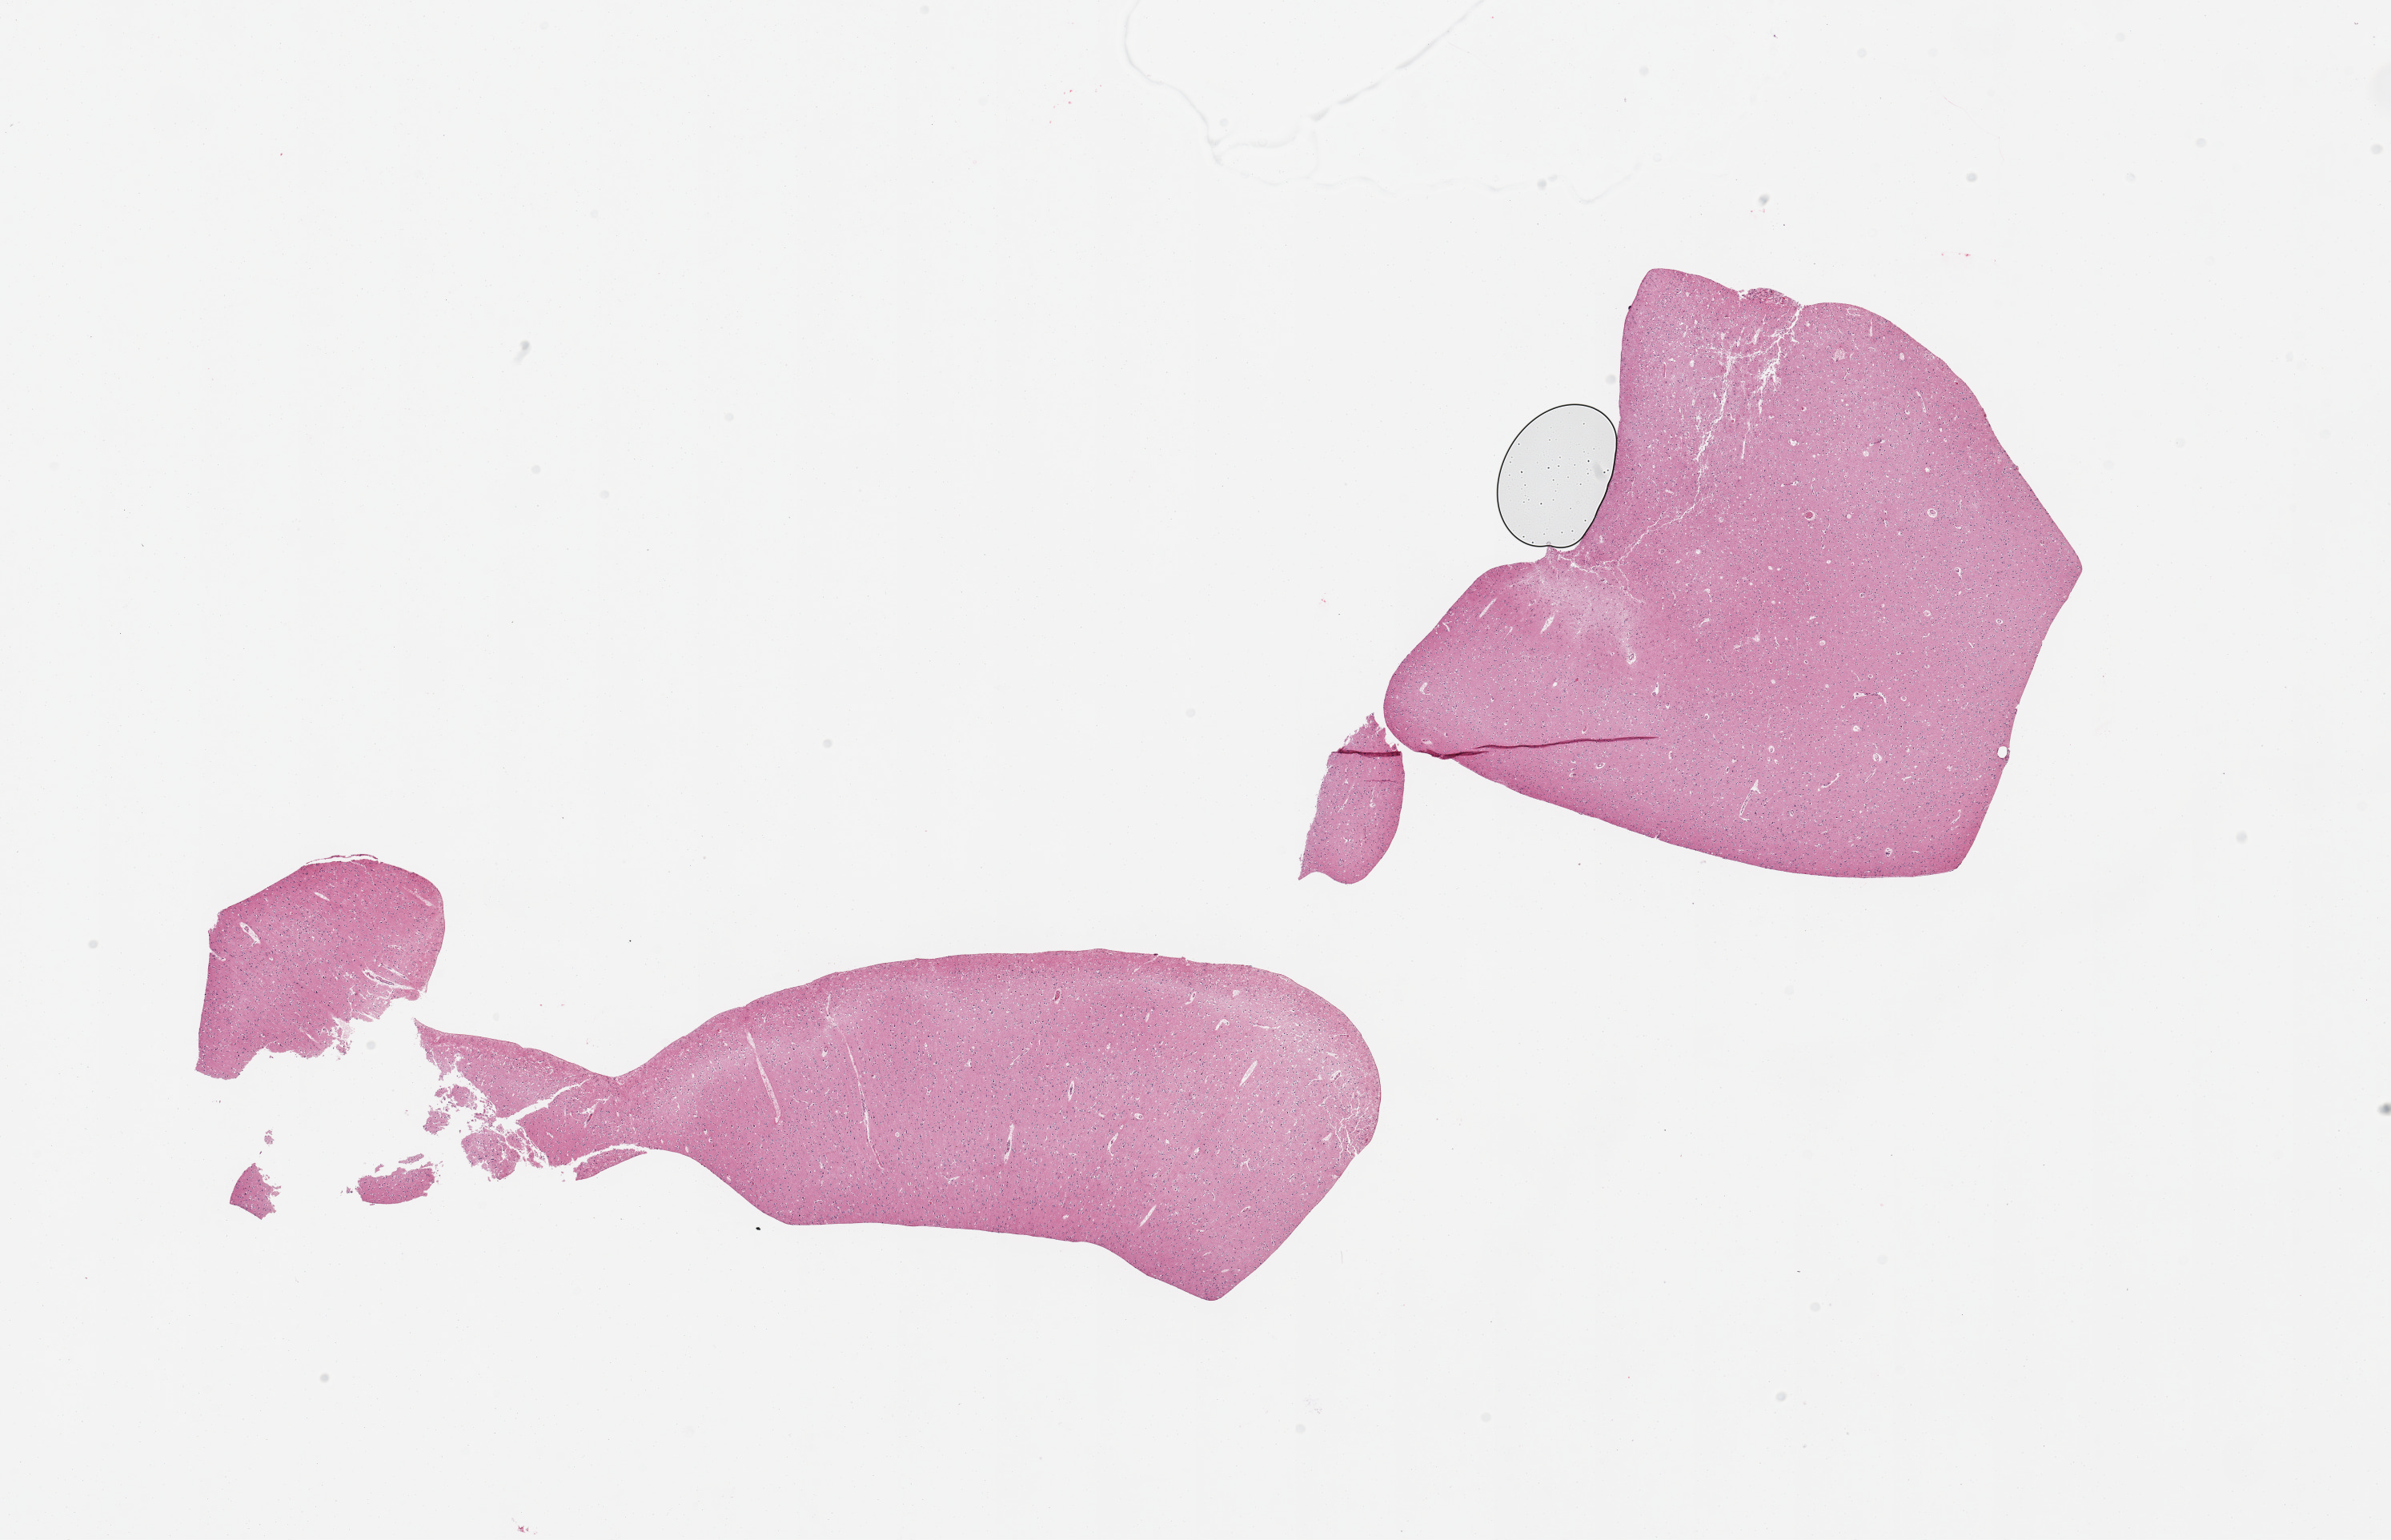
Digitized haematoxylin and eosin-stained section, brightfield — a low-resolution overview of the entire scanned area, about 23.6 x 15.2 mm (slide scanned at 20x); PAXgene-fixed, paraffin-embedded tissue; section of cerebral cortex (target tissue); donor tissue sample.
Reviewer comment on this tissue sample: 2 pieces, no abnormalities.